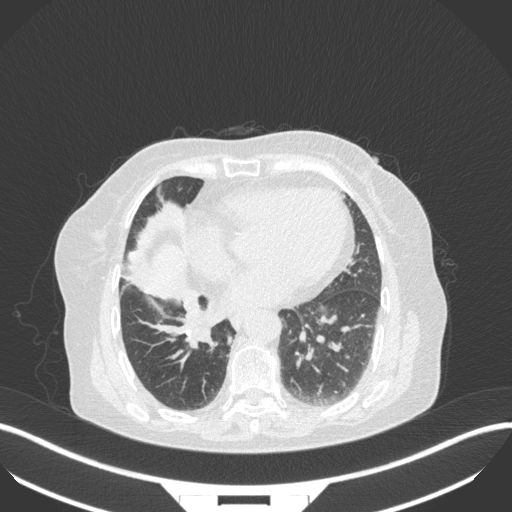
Chest CT, one axial slice; position 118 of 329 along the scan axis; reconstruction kernel B31f; 120 kVp; lung window (W 1500 / L -600 HU); 1 mm slice thickness; 512 × 512 image matrix, field of view 400 × 400 mm. Patient: female, 75 years. Case-level facts recorded for this patient, not image findings: clinical TNM (as recorded): T1b N0 M1a; histopathological grade: G1.
Annotated regions visible in this slice (bounding box drawn by a radiologist):
- lung tumour (recorded histology: squamous cell carcinoma): box from (x=179, y=305) to (x=215, y=351) px